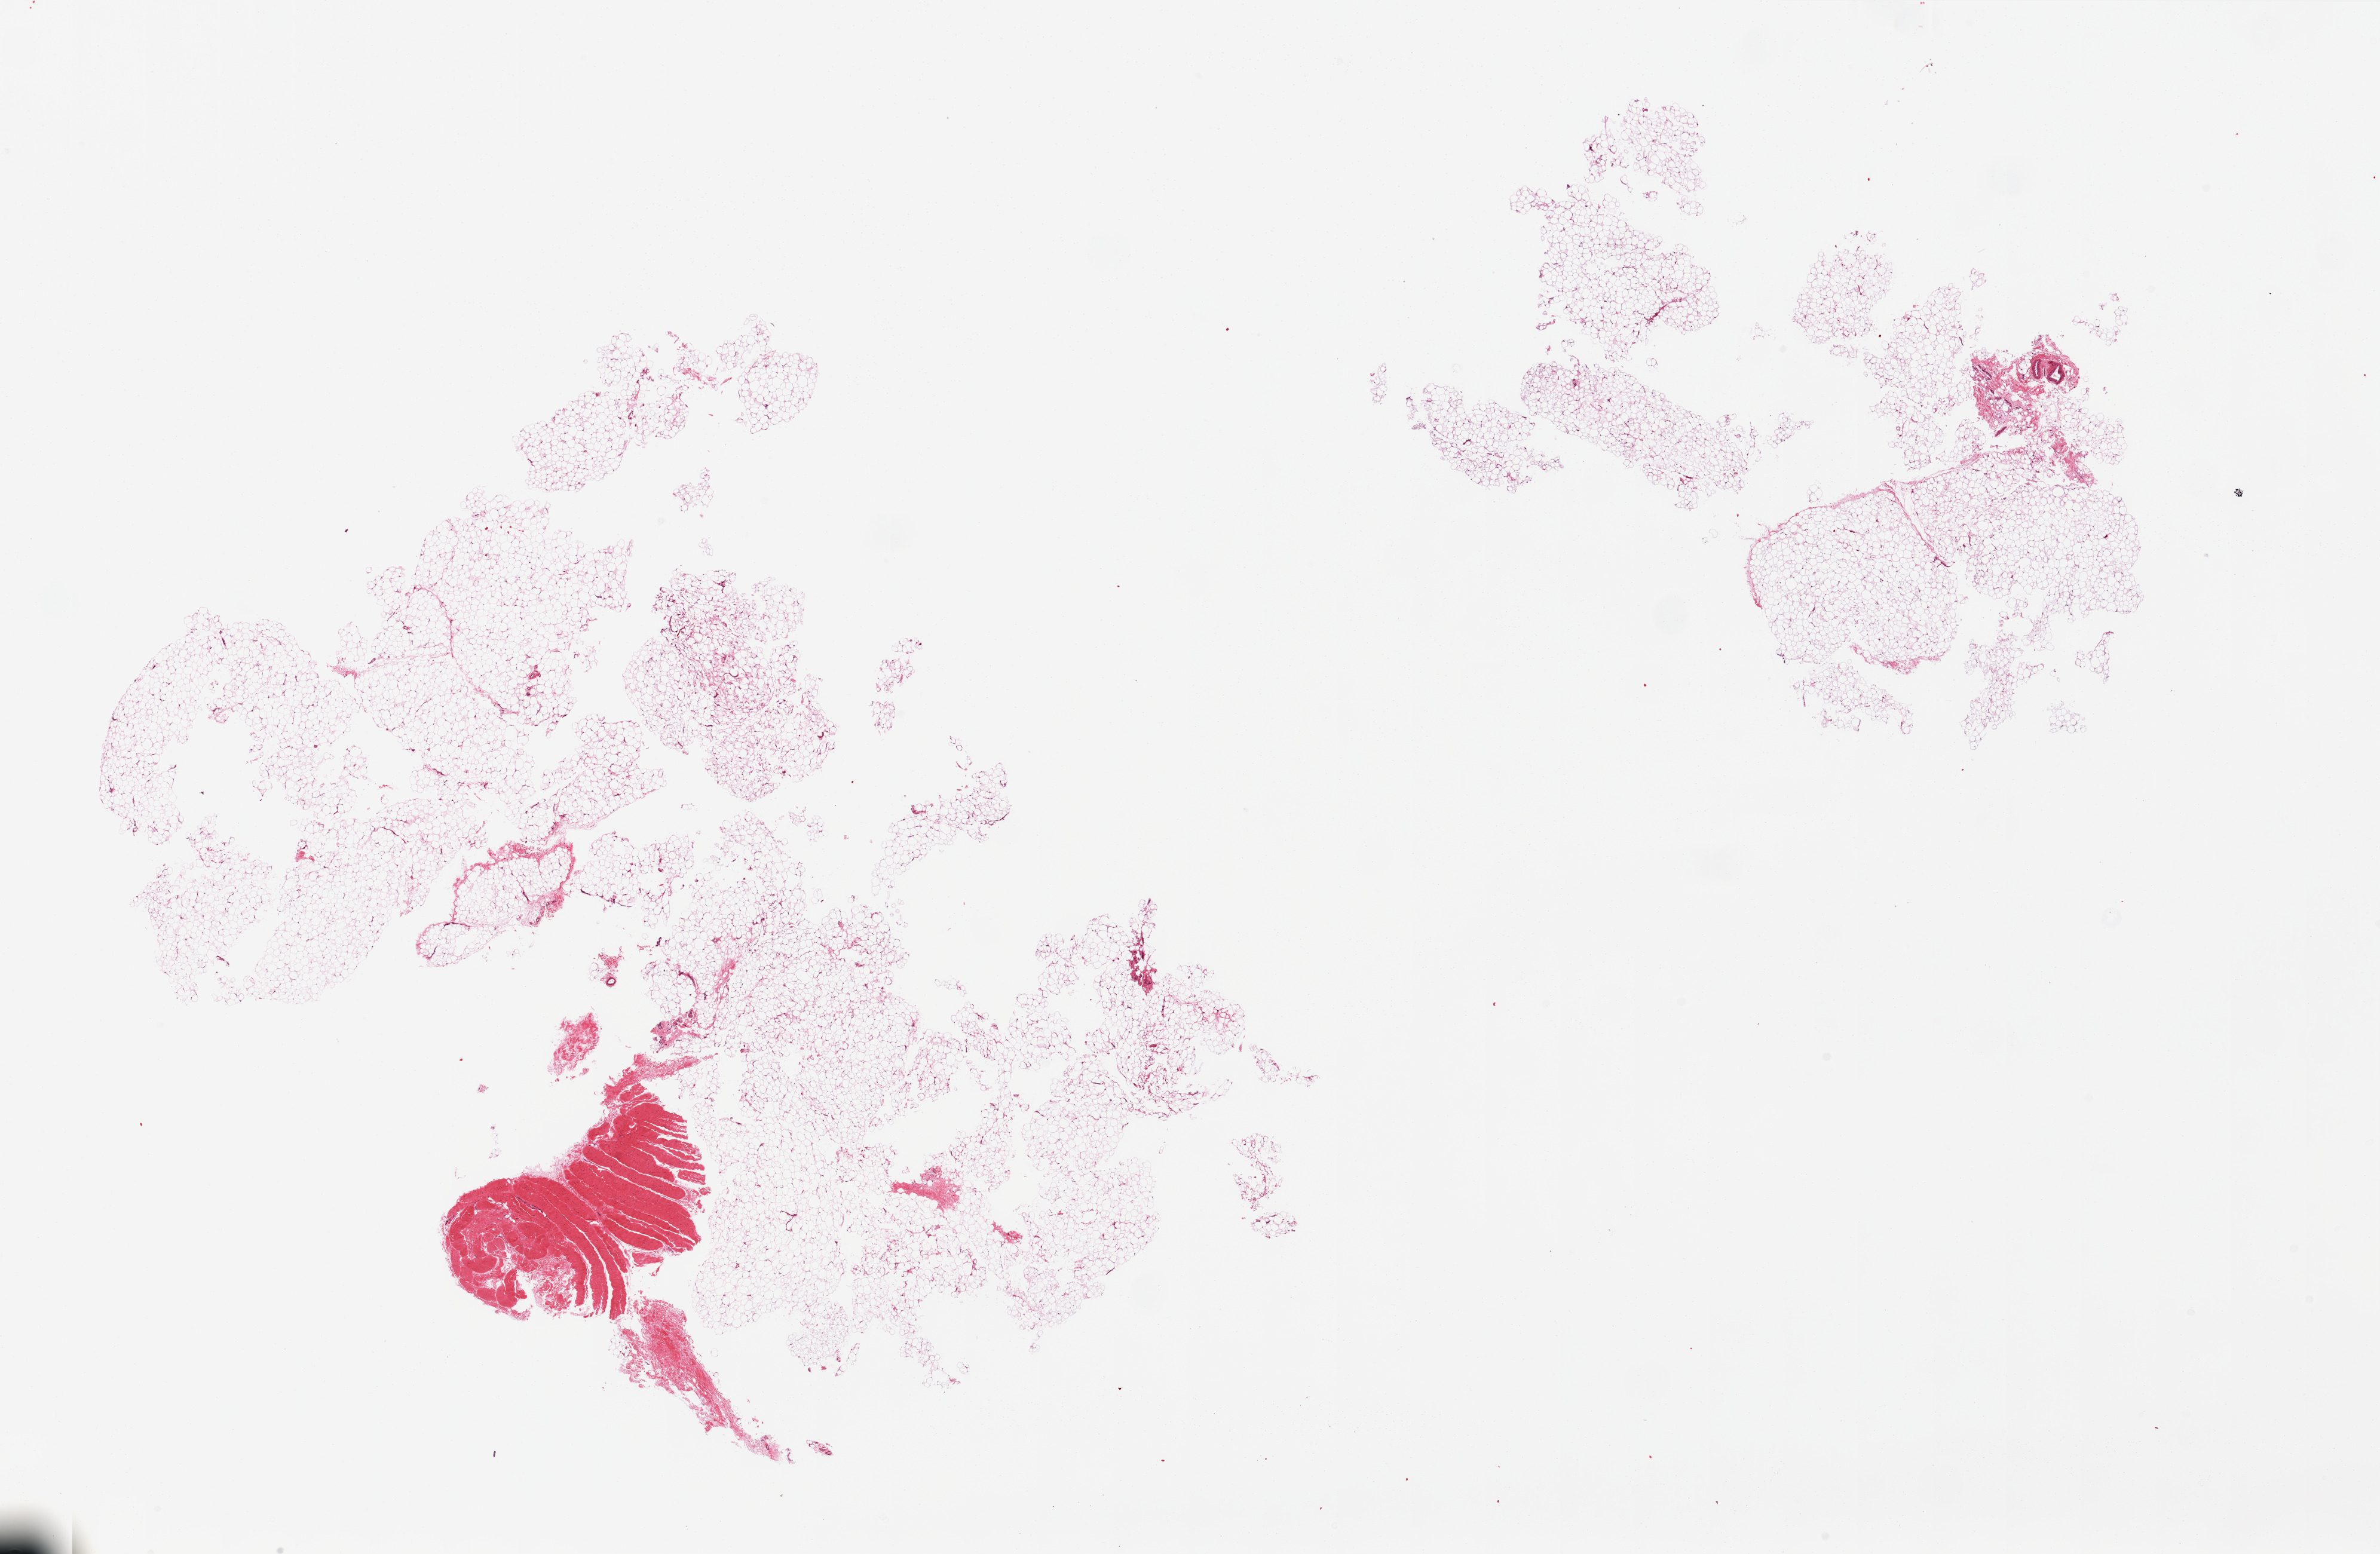
Digitized hematoxylin and eosin (H&E)-stained section — shown as a low-resolution overview of the whole scanned area (about 31.5 x 20.6 mm); PAXgene-fixed, paraffin-embedded tissue; target tissue: adipose tissue; donor tissue sample. Female donor.
Reviewer comment on this tissue sample: 2 pieces, focal fascia.